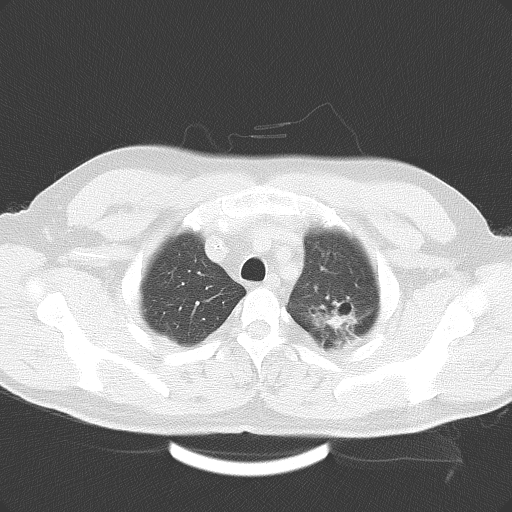
Chest CT, one axial slice; slice 33 of 41 in the series (ordered by position); lung window (W 1500 / L -600 HU); 512 × 512 image matrix, field of view 362 × 362 mm. Patient: male, 45 years. Case-level facts recorded for this patient, not image findings: clinical TNM (as recorded): T2 N0 M0.
Structures marked on this image (bounding box drawn by a radiologist):
- lung tumour (recorded histology: adenocarcinoma): box from (x=303, y=290) to (x=366, y=352) px